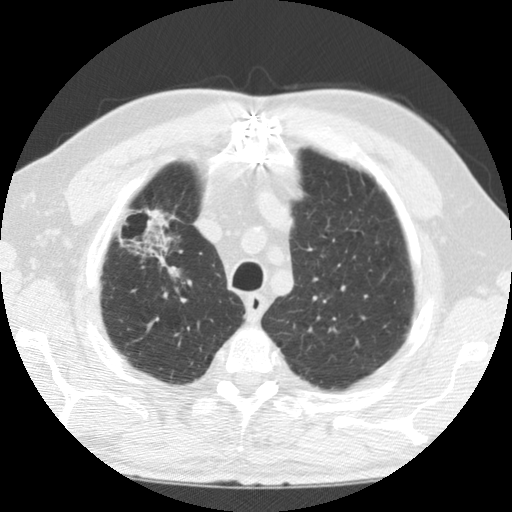
Low-dose screening chest CT, axial slice; first (baseline) screen; lung window (W 1500 / L -600 HU); 2.5 mm slice thickness. Male, age 69 years at enrolment.
• Expert-annotated lung lesion, bounding box [x1, y1, x2, y2] px = [104, 210, 195, 293].
• Screening reader's record for this exam: no non-calcified nodule ≥4 mm recorded.
• Official screen result: negative screen, minor abnormalities not suspicious for lung cancer.
• Later outcome: lung cancer diagnosed 171 days after this screen — adenocarcinoma, NOS, right upper lobe, poorly differentiated (G3), stage IIIB (AJCC 6th edition), 40 mm at pathology.